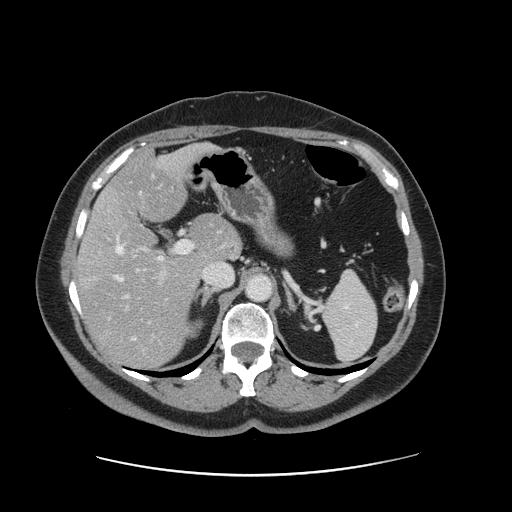
Contrast-enhanced abdominal CT, one axial slice. Slice 89 of 161 in the series (ordered by position). Intravenous contrast given. Soft-tissue window (W 400 / L 40 HU). 512 × 512 image matrix. Female patient, age 62 years. Case-level facts recorded for this patient, not image findings: diagnosis: colorectal cancer liver metastases, imaged before liver resection; multiple liver metastases: no.
Outlined on this slice (manually delineated by an expert):
- hepatic veins: box from (x=115, y=192) to (x=142, y=340) px
- liver: (x=78, y=145)–(x=240, y=367)
- planned liver remnant (the part of the liver to remain after resection): (x=108, y=145)–(x=239, y=265)
- portal vein (with intrahepatic branches): (x=122, y=241)–(x=193, y=339)